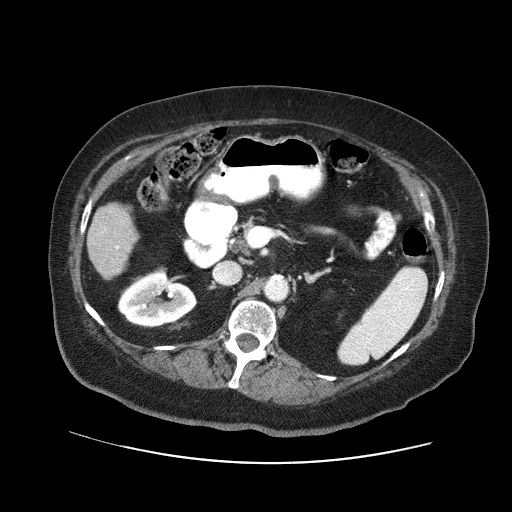
Contrast-enhanced abdominal CT (liver protocol), one axial slice; position 14 of 71 along the scan axis; reconstruction kernel STANDARD; 120 kVp; soft-tissue window (W 400 / L 40 HU); 2.5 mm slice thickness; 512 × 512 image matrix, field of view 400 × 400 mm. From the clinical record (not read from this slice): diagnosis: hepatocellular carcinoma (patient treated with transarterial chemoembolisation; whether this scan precedes or follows treatment is not stated here); TNM stage (as recorded): Stage-II; Child-Pugh class: A; tumour differentiation: poorly differentiated; tumour nodularity: multinodular.
Annotated regions visible in this slice (semi-automatically segmented with operator editing):
- liver parenchyma outside the tumour (the mass and vessels are separate outlines, so this box may not span the whole liver): bounding box (x1, y1, x2, y2) in pixels: (86, 202, 138, 280)
- liver vessels: (116, 246, 119, 249)